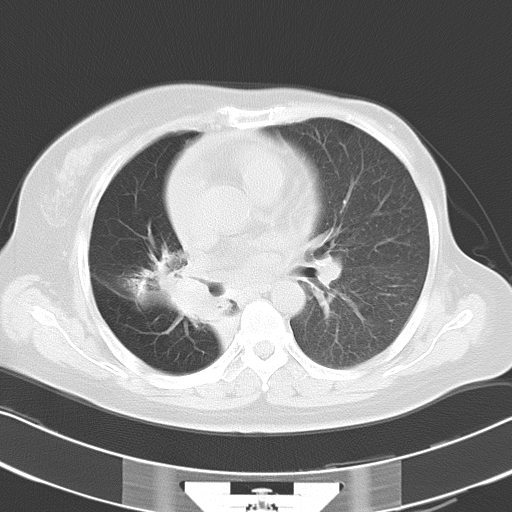
Chest CT, one axial slice; position 17 of 30 along the scan axis; reconstruction kernel B70f; 120 kVp; lung window (W 1500 / L -600 HU); 8 mm slice thickness; 512 × 512 image matrix. Patient: female, 53 years. Case-level facts recorded for this patient, not image findings: clinical TNM (as recorded): T2b N1 M0.
Outlined on this slice (rectangle marked by the reading radiologist):
- lung tumour (recorded histology: adenocarcinoma): bounding box <122,244,233,323> (left, top, right, bottom; pixels)